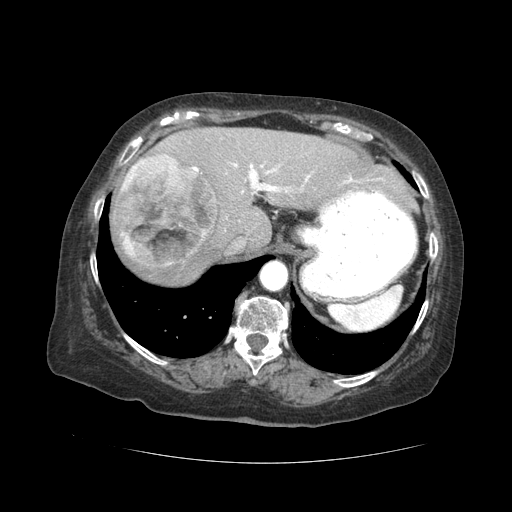
Contrast-enhanced abdominal CT (liver protocol), one axial slice. Slice 34 of 59 in the series (ordered by position). Reconstruction kernel STANDARD. Soft-tissue window (W 400 / L 40 HU). 2.5 mm slice thickness. 512 × 512 image matrix, field of view 380 × 380 mm. Case-level facts recorded for this patient, not image findings: diagnosis: hepatocellular carcinoma (patient treated with transarterial chemoembolisation; whether this scan precedes or follows treatment is not stated here); TNM stage (as recorded): Stage-I; Child-Pugh class: A.
Structures marked on this image (semi-automatically segmented with operator editing):
- abdominal aorta: box from (x=261, y=263) to (x=287, y=290) px
- liver parenchyma outside the tumour (the mass and vessels are separate outlines, so this box may not span the whole liver): (x=110, y=126)–(x=406, y=284)
- mass: (x=117, y=154)–(x=218, y=269)
- liver vessels: (x=192, y=163)–(x=379, y=194)